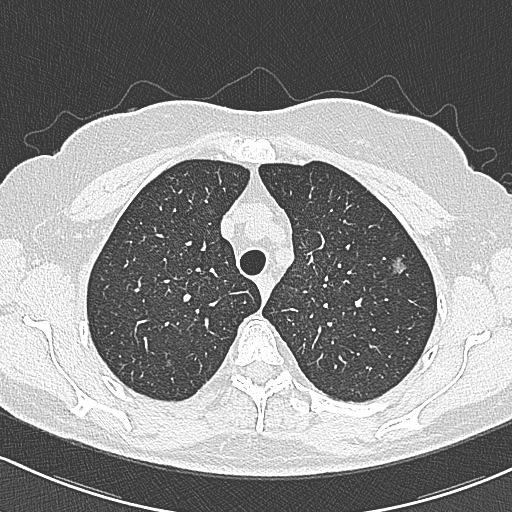
Chest CT (low-dose screening protocol), one axial image; baseline annual screen; lung window (W 1500 / L -600 HU); slice 68 of 312 in the series; 512 × 512 image matrix, field of view 318 × 318 mm. Female participant, aged 65 years at enrolment. Current smoker at enrolment.
• Expert-annotated lung lesion, bounding box [x1, y1, x2, y2] px = [380, 249, 417, 286].
• The screening reader recorded 3 non-calcified nodules or masses ≥4 mm on this exam; which of them this box marks is not recorded.
• Official screen result: positive, change unspecified: nodule(s) >= 4 mm or enlarging nodule(s), mass(es), or other non-specific abnormalities suspicious for lung cancer.
• Lung cancer was diagnosed 390 days after this screen: bronchiolo-alveolar carcinoma, non-mucinous, left upper lobe, stage IA (AJCC 6th edition), 10 mm at pathology.